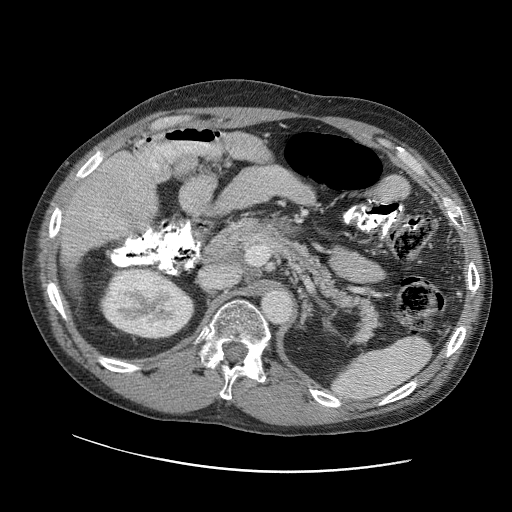
Contrast-enhanced abdominal CT (liver protocol), one axial slice; position 56 of 109 along the scan axis; reconstruction kernel STANDARD; 120 kVp; soft-tissue window (W 400 / L 40 HU); 2.5 mm slice thickness; 512 × 512 image matrix, field of view 400 × 400 mm. From the clinical record (not read from this slice): diagnosis: hepatocellular carcinoma (patient treated with transarterial chemoembolisation; whether this scan precedes or follows treatment is not stated here); TNM stage (as recorded): Stage-IIIC; Child-Pugh class: B; tumour differentiation: well differentiated.
Annotated regions visible in this slice (semi-automatically segmented with operator editing):
- liver parenchyma outside the tumour (the mass and vessels are separate outlines, so this box may not span the whole liver): box from (x=58, y=149) to (x=156, y=286) px
- liver vessels: (x=127, y=154)–(x=144, y=181)